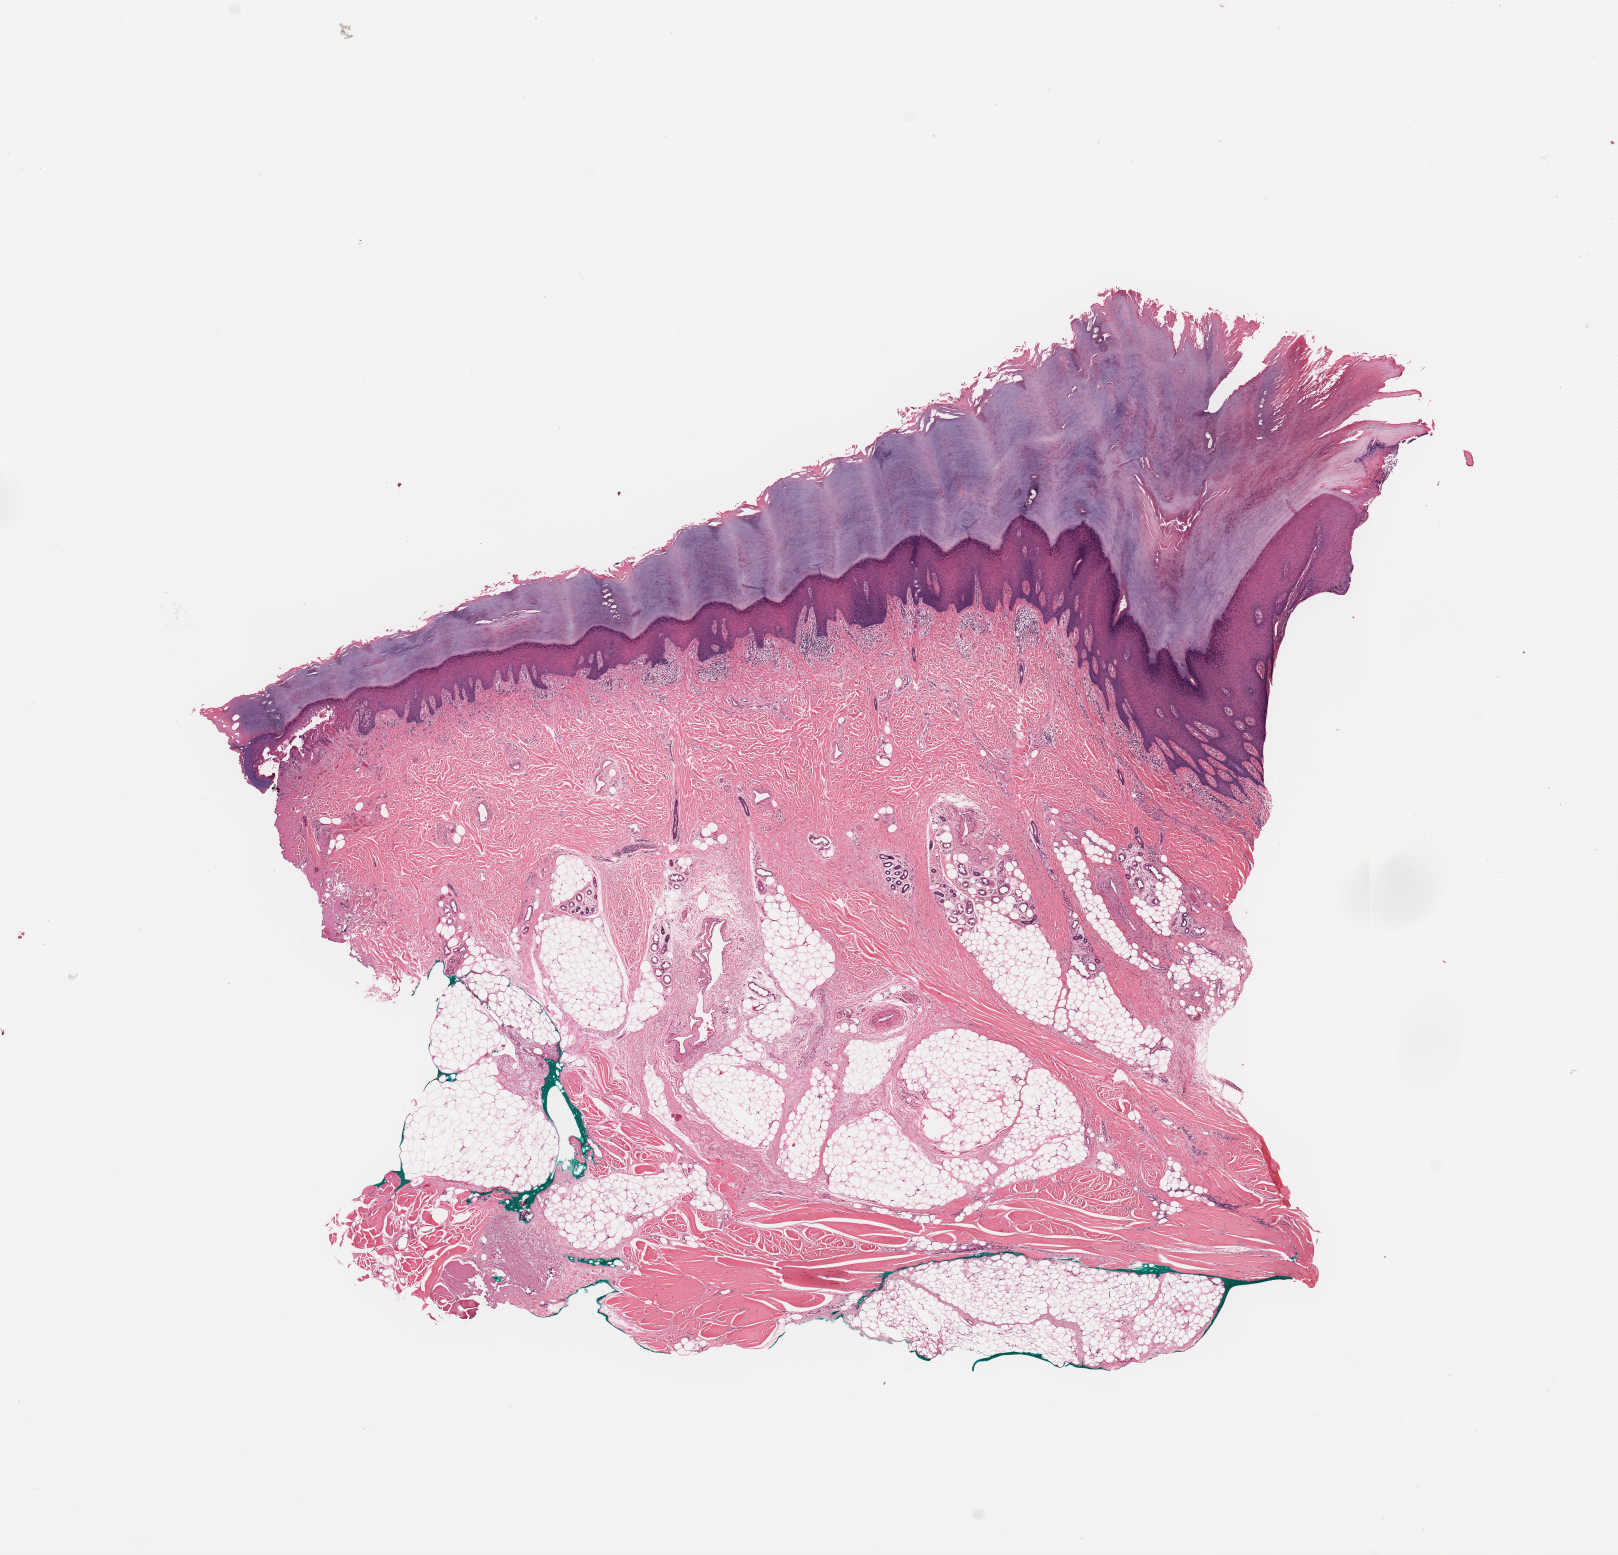
Whole-slide histology image, Hematoxylin and eosin (H&E) stained, whole scanned area (about 12.8 x 12.3 mm) shown as a low-resolution overview; normal (non-tumour) tissue sample, sampled site: skin. Male, 71 y/o.
* this section: normal (non-tumour) tissue from the same patient
* patient diagnosis: Malignant melanoma, NOS